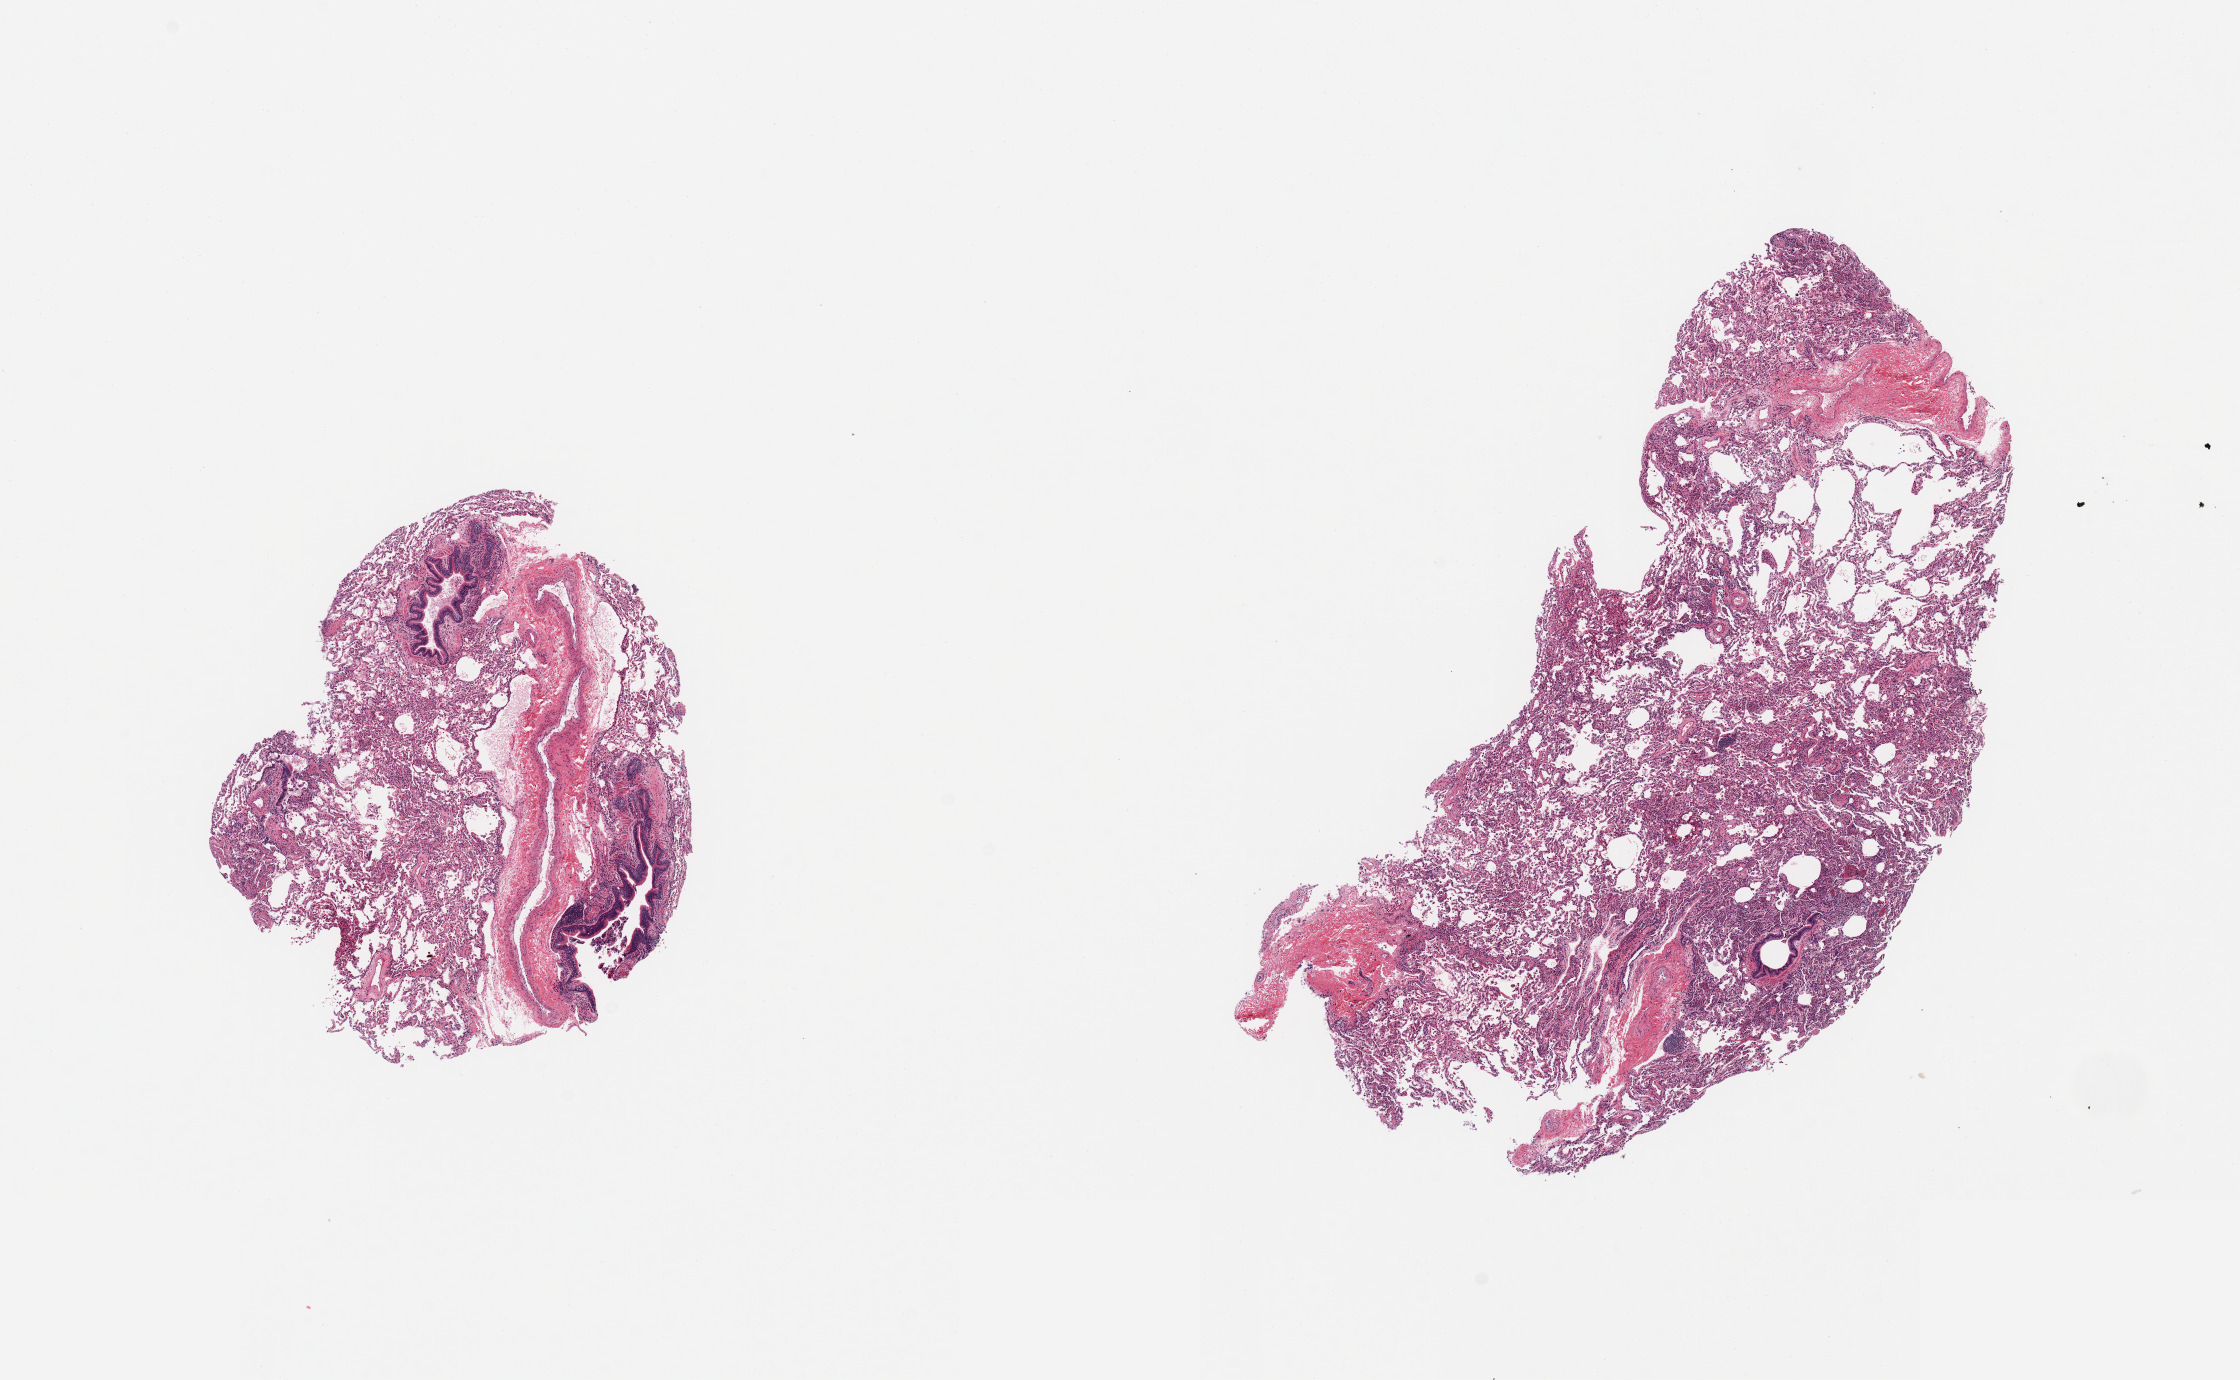
Haematoxylin and eosin whole-slide image, brightfield — whole scanned area (about 17.7 x 10.9 mm, from a 20x scan) shown as a low-resolution overview, PAXgene-fixed paraffin-embedded (PFPE) section, sampled site (target tissue): lung, tissue donor sample. Male donor.
Review note (as recorded): 2 pieces; collapse, reactive changes with mild acute inflammation.